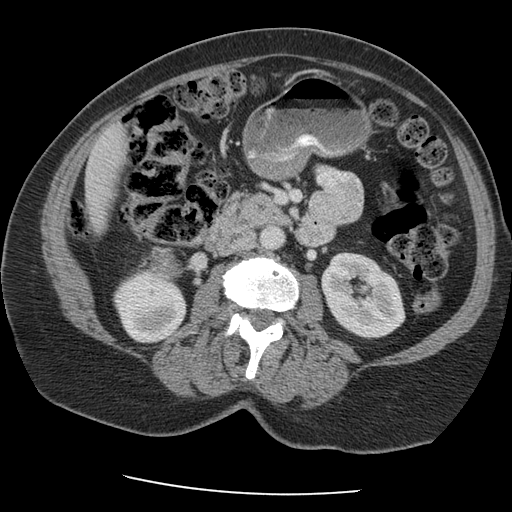
Contrast-enhanced abdominal CT, one axial slice; position 102 of 163 along the scan axis; intravenous contrast given; soft-tissue window (W 400 / L 40 HU); 512 × 512 image matrix. Patient: female, 70 years. From the clinical record (not read from this slice): diagnosis: adrenocortical carcinoma; tumour side: right adrenal; tumour size at pathology: 9.5 cm; Ki-67 index: 5 %; stage (as recorded): 2.
Annotated regions visible in this slice (semi-automatically segmented with operator editing):
- mass: bounding box (x1, y1, x2, y2) in pixels: (153, 250, 180, 274)